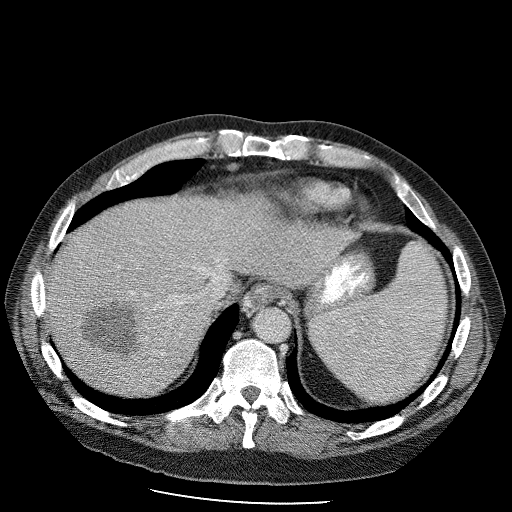
Contrast-enhanced abdominal CT (liver protocol), one axial slice. Slice 85 of 98 in the series (ordered by position). Soft-tissue window (W 400 / L 40 HU). 2.5 mm slice thickness. 512 × 512 image matrix, field of view 400 × 400 mm. From the clinical record (not read from this slice): diagnosis: hepatocellular carcinoma (patient treated with transarterial chemoembolisation; whether this scan precedes or follows treatment is not stated here); TNM stage (as recorded): Stage-II; Child-Pugh class: B.
Structures marked on this image (semi-automatically segmented with operator editing):
- liver parenchyma outside the tumour (the mass and vessels are separate outlines, so this box may not span the whole liver): bounding box [x1, y1, x2, y2] px = [44, 198, 325, 390]
- mass: [77, 291, 151, 360]